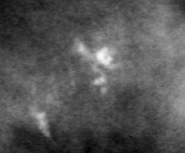
Crop from a digitized film mammogram around one marked abnormality; right breast; CC view; BI-RADS breast density category 3 (scale 1–4).
- Finding: calcifications, morphology pleomorphic, distribution clustered; BI-RADS assessment category 4; pathology result (as recorded, not read from the image): benign.